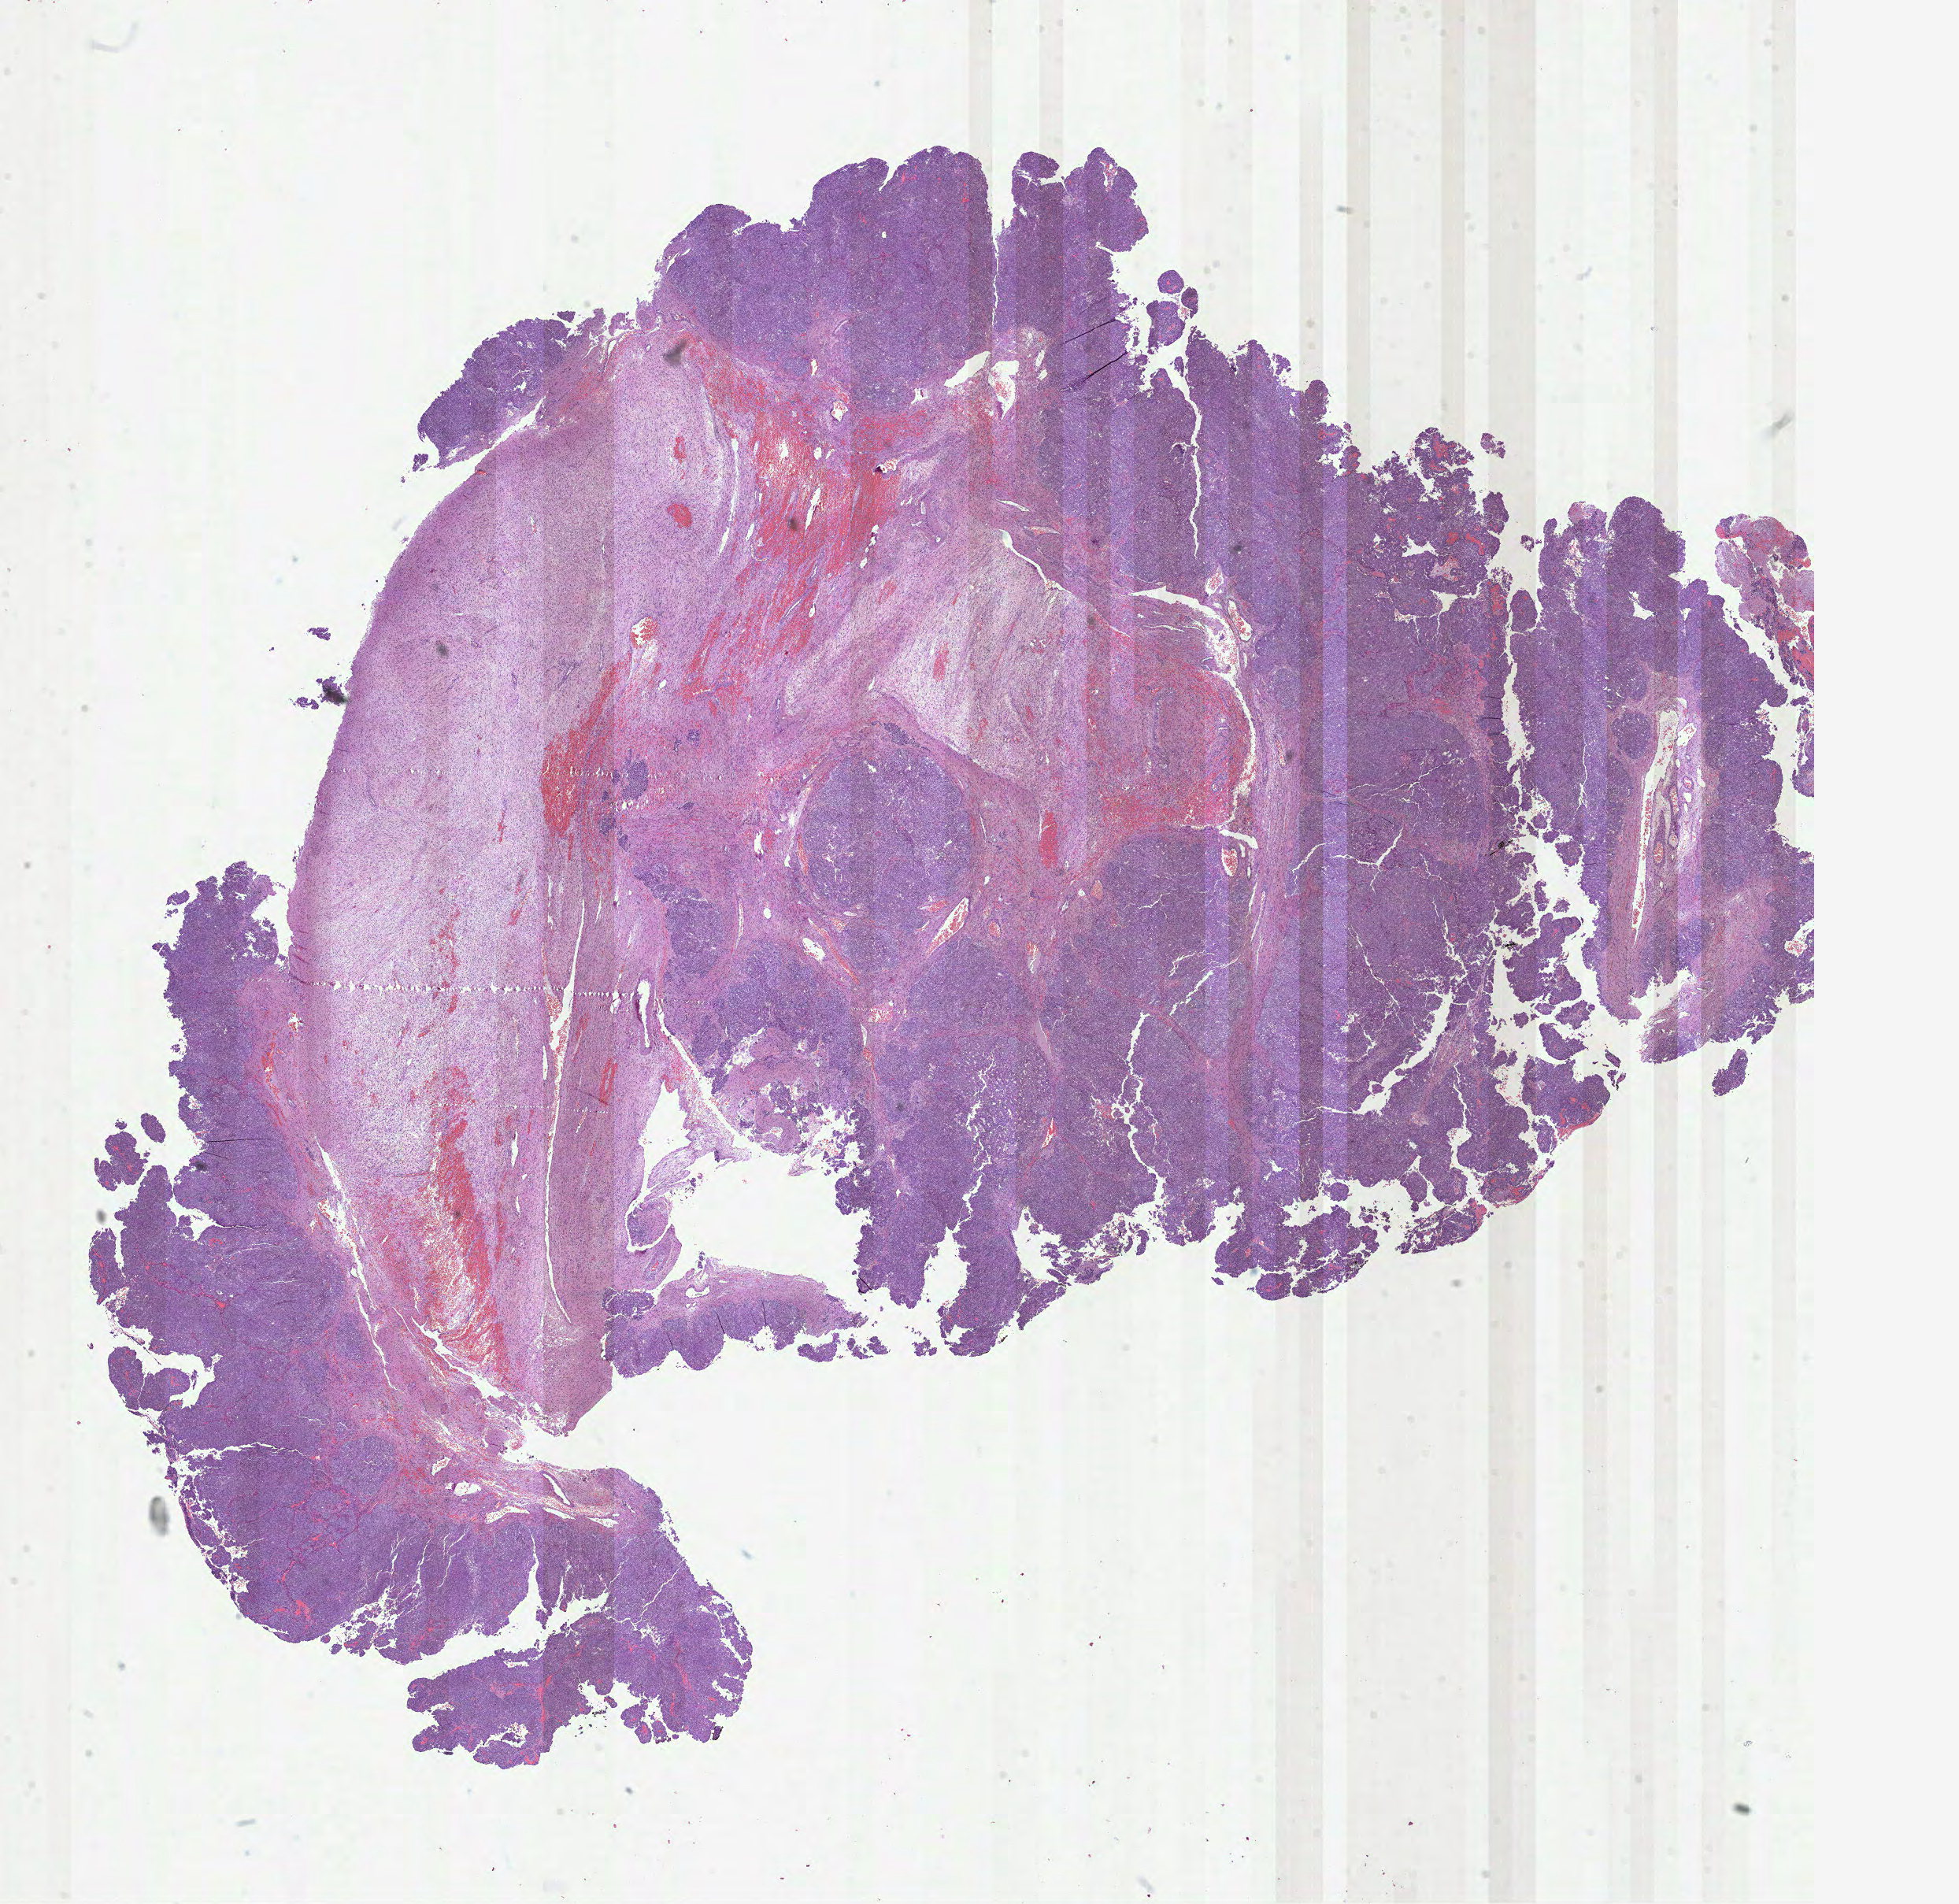
Digitized Hematoxylin and eosin (H&E) stained tissue section (whole slide), whole scanned area (about 20.1 x 19.5 mm) shown as a low-resolution overview, FFPE section, sample: primary tumour, ovary. Female, age 62 years at initial diagnosis. Histologic grade: G3 (poorly differentiated).
• FIGO stage: IC
• pathologic diagnosis: Serous cystadenocarcinoma, NOS